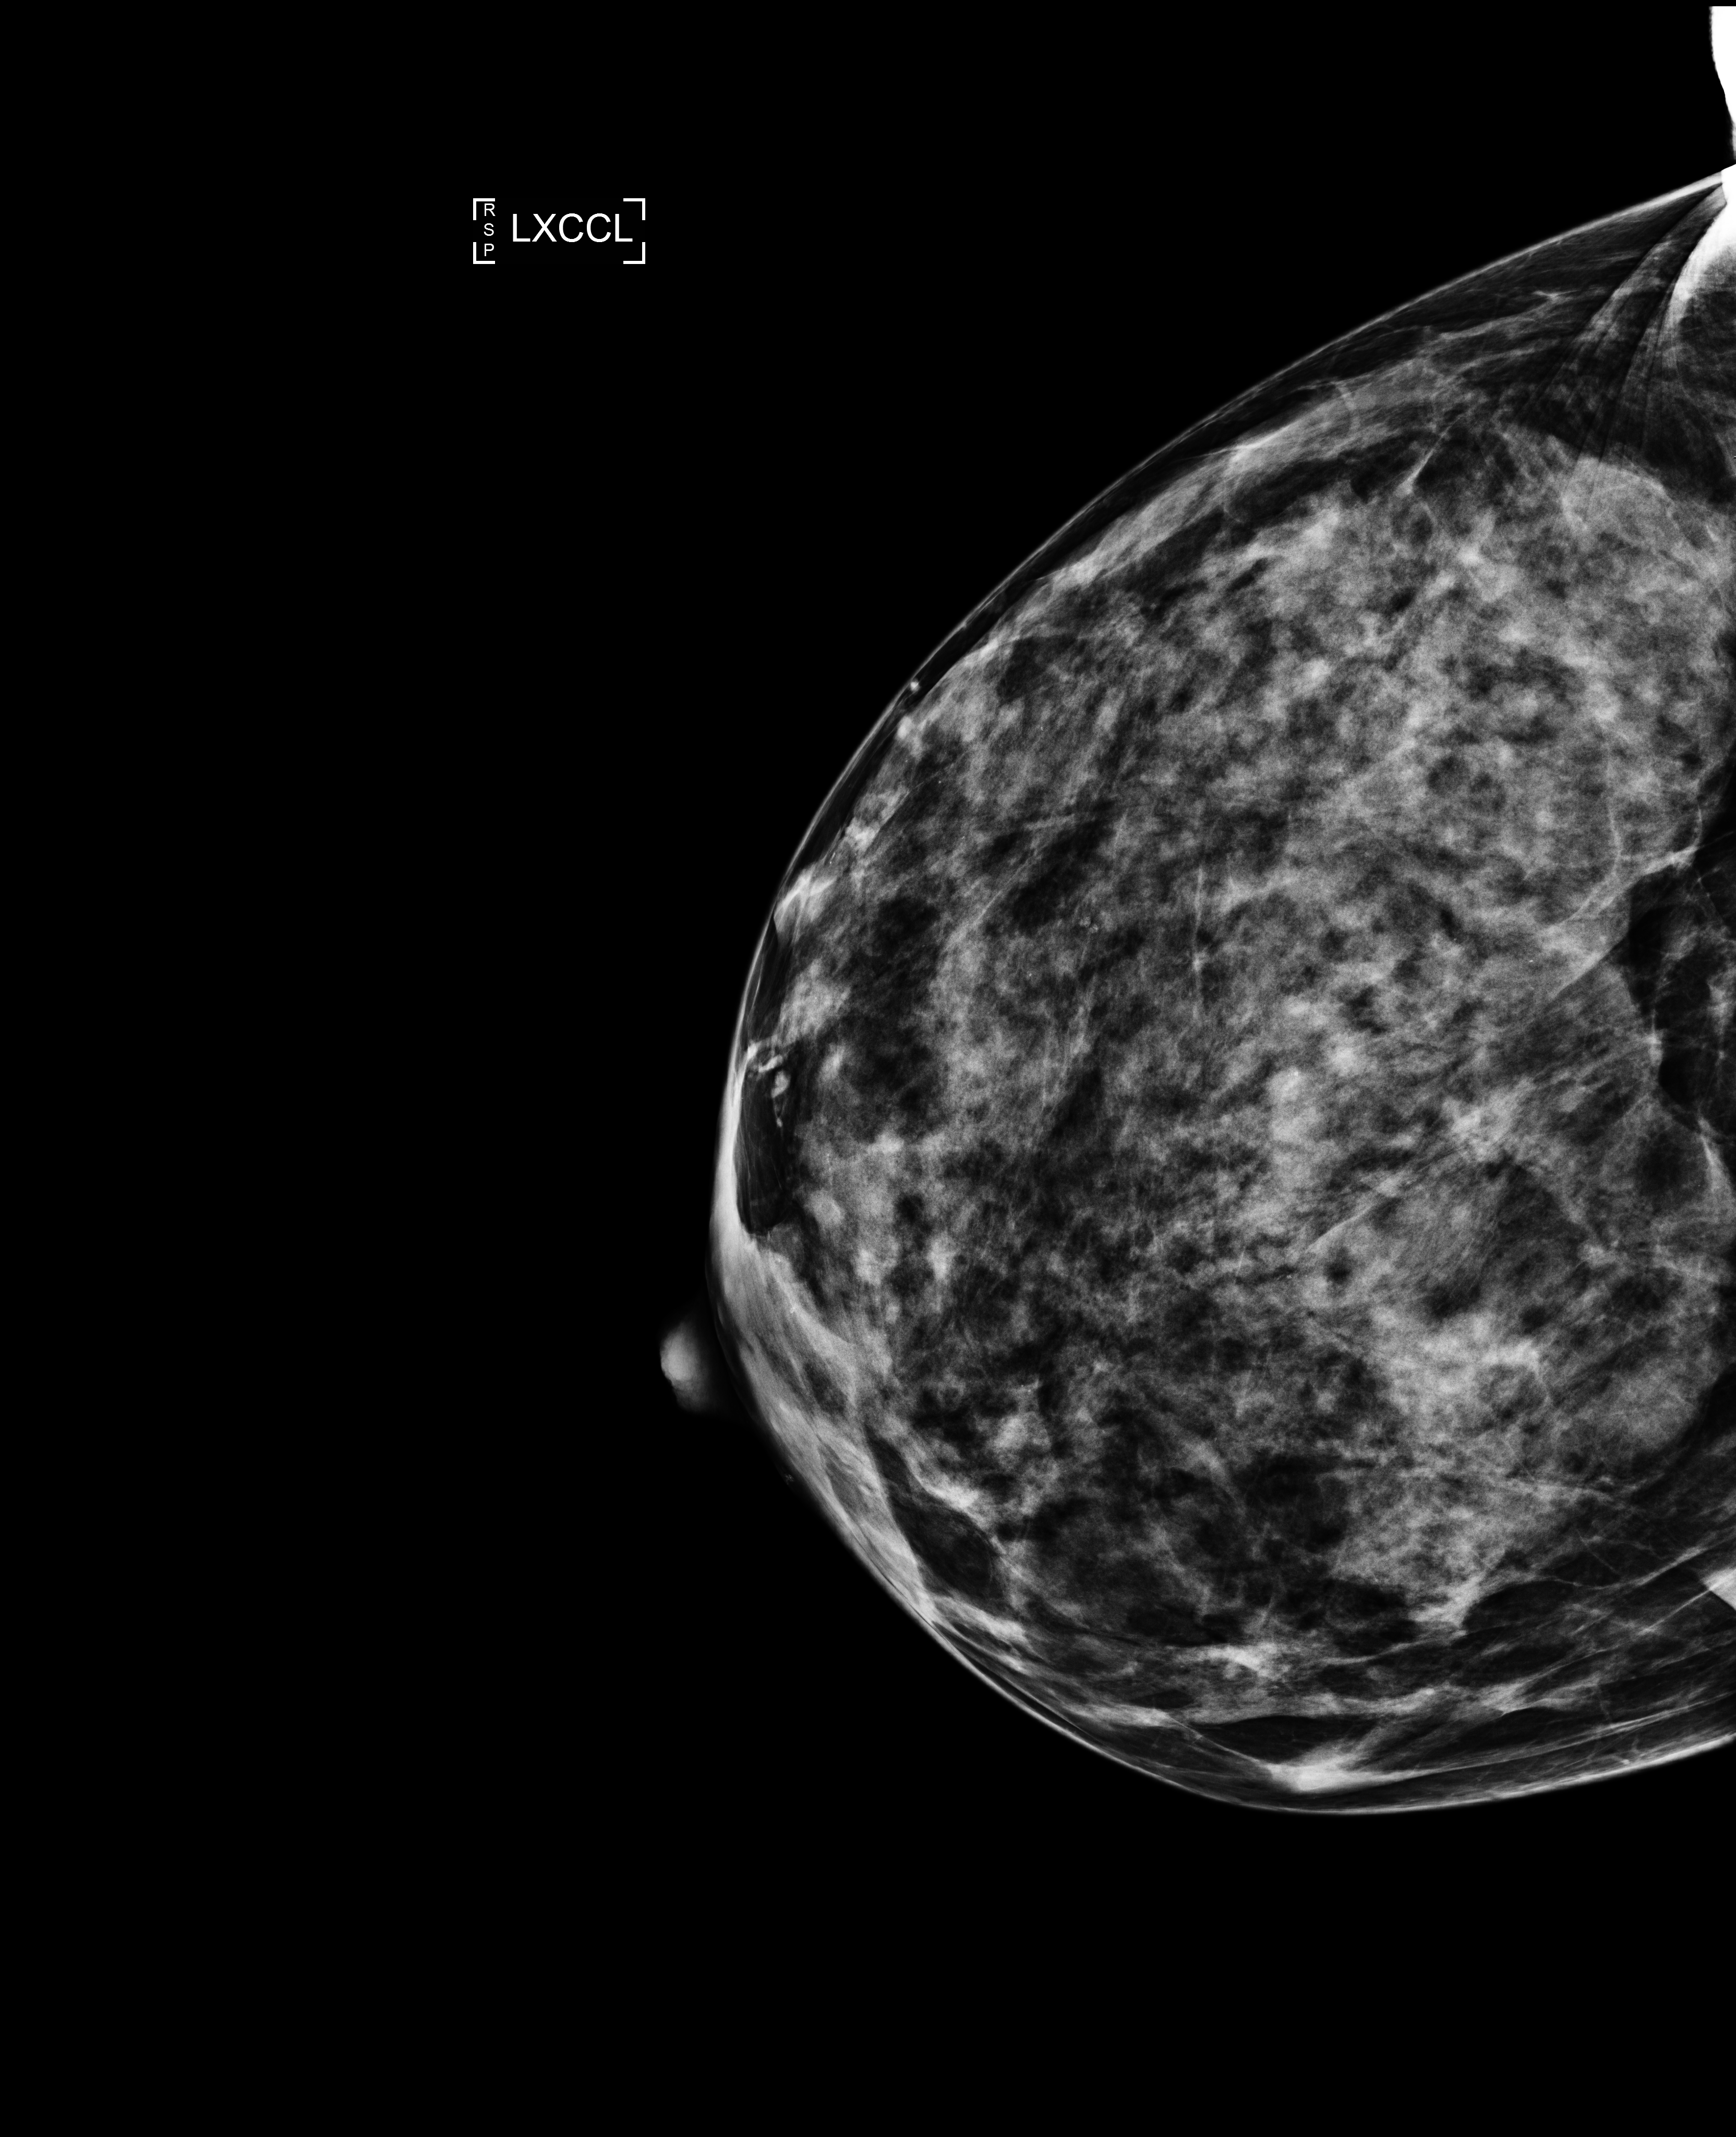
Full-field digital mammogram (FFDM); left breast; laterally exaggerated craniocaudal (XCCL) view; annual screening mammography examination; compressed breast thickness 61 mm. Female patient, age 51 years.
Final BI-RADS category for the screening round (tomosynthesis exam, both breasts): category 2.